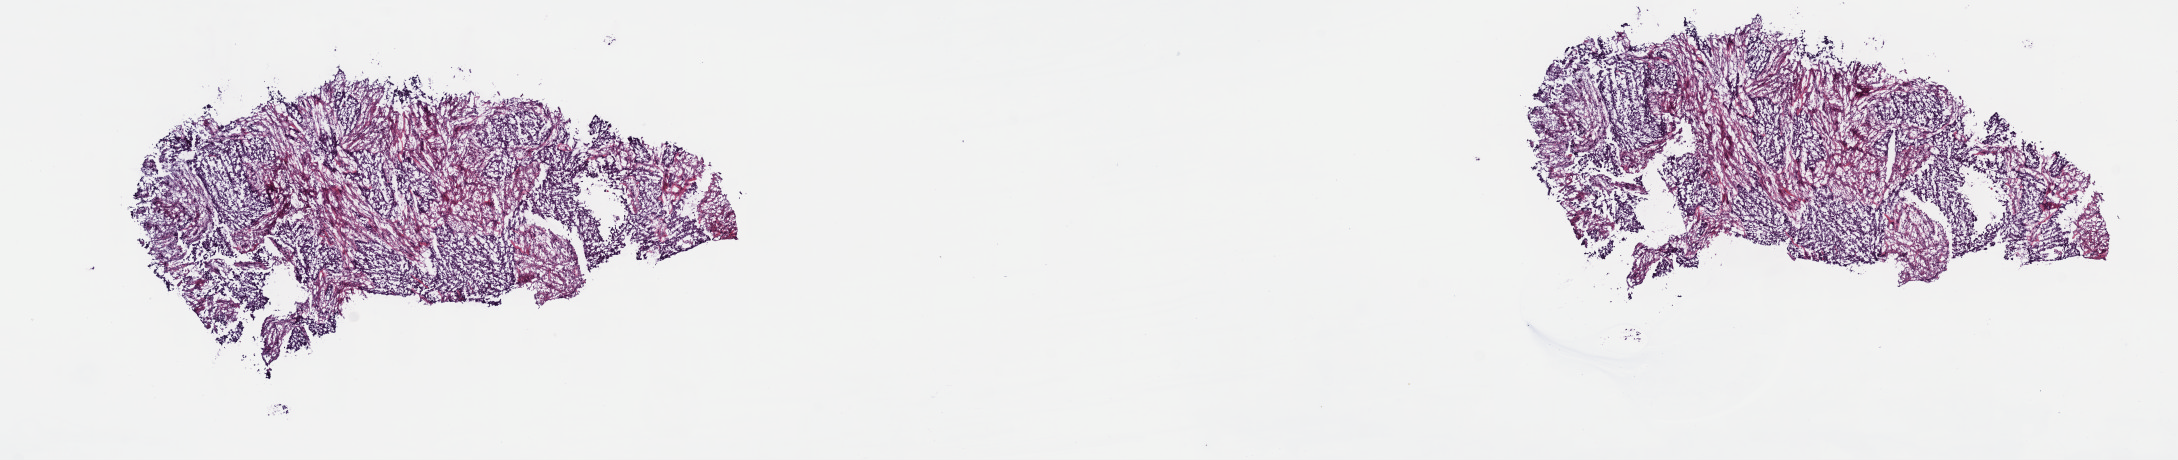
Digitized H&E tissue section (whole slide) — low-resolution overview of the scanned area, about 17.6 x 3.7 mm (slide scanned at 40x); frozen section from the top of the tissue portion; bladder, primary tumour sample. Patient sex: male. Histologic grade: high grade. Composition of this section per pathologist review: tumour cells 100%, tumour nuclei 65%, normal cells 0%, stromal cells 0%, necrosis 0%. Infiltration values recorded for this section: lymphocyte infiltration 3%, monocyte infiltration 0%, neutrophil infiltration 0%.
Diagnosis: Transitional cell carcinoma (posterior wall of bladder). AJCC pathologic stage: II (6th edition).